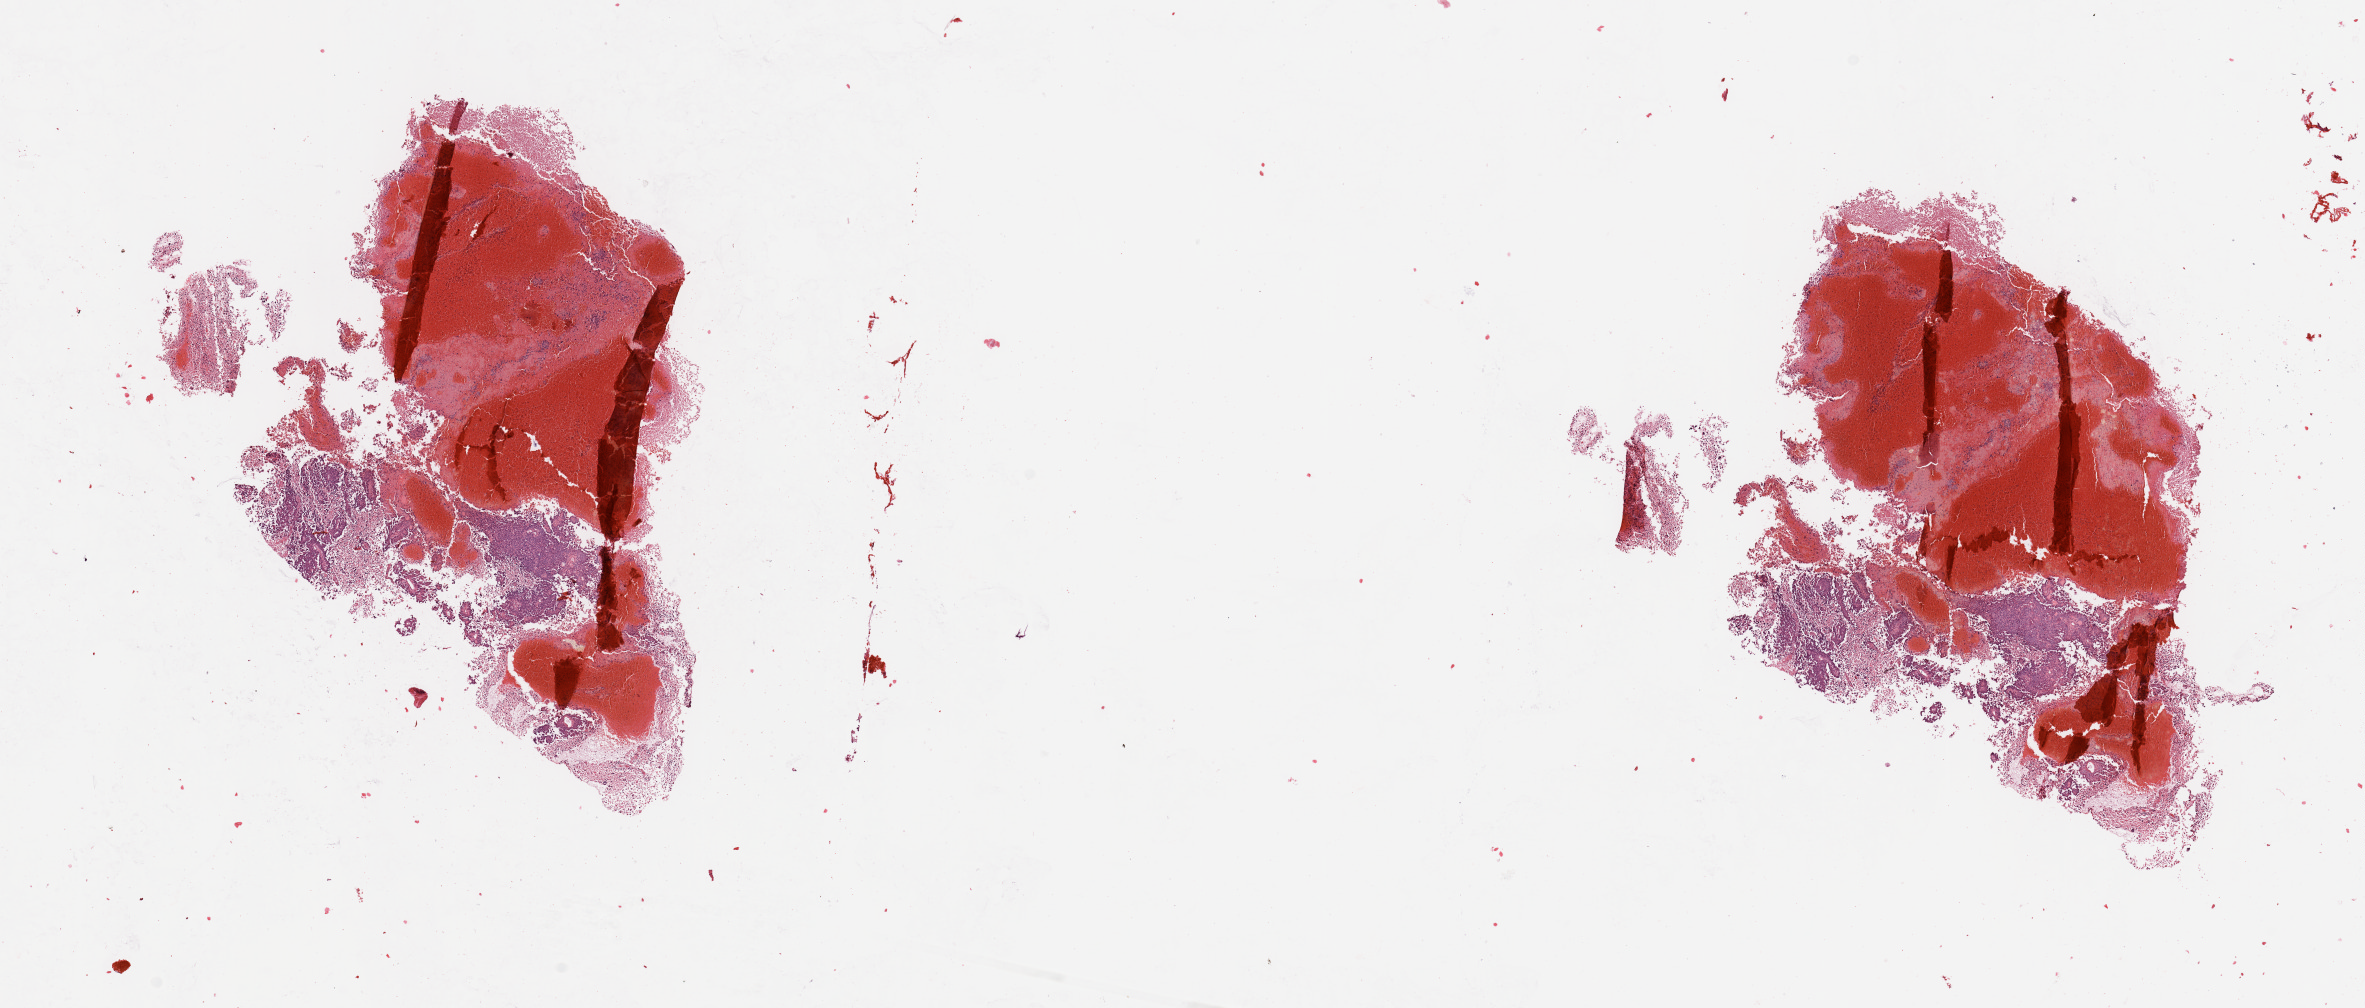
Digitized H&E-stained tissue section (whole slide), shown as a low-resolution overview of the whole scanned area (about 18.7 x 8.0 mm). Tumour tissue sample, sampled site: frontal lobe. Female, 60 y/o. Composition of this section per pathologist review: tumour nuclei 60%, necrosis 35%.
* primary tumour site (as recorded): frontal lobe
* histologic diagnosis: Glioblastoma